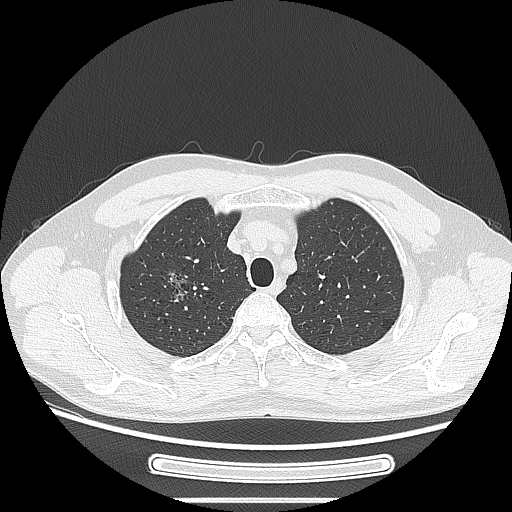
Chest CT, one axial slice; slice 217 of 269 in the series (ordered by position); reconstruction kernel LUNG; lung window (W 1500 / L -600 HU); 512 × 512 image matrix, field of view 382 × 382 mm. Patient: male, 53 years. From the clinical record (not read from this slice): clinical TNM (as recorded): T1c N0 M0.
Outlined on this slice (bounding box drawn by a radiologist):
- lung tumour (recorded histology: adenocarcinoma): bounding box [x1, y1, x2, y2] px = [163, 259, 192, 314]